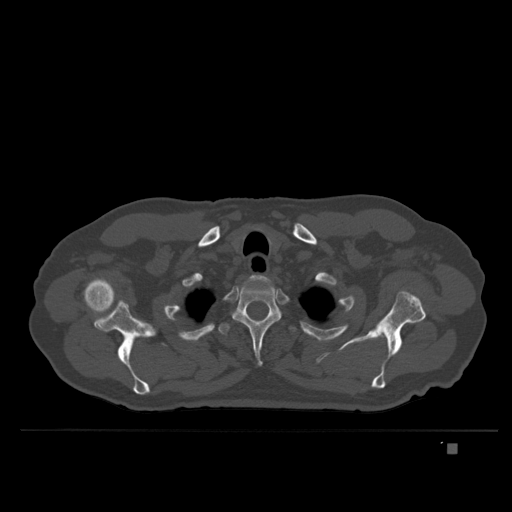
CT including the spine, one axial slice. Position 312 of 435 along the scan axis. Bone window (W 1800 / L 400 HU). 1.5 mm slice thickness. 512 × 512 image matrix, field of view 434 × 434 mm. Patient: male, 73 years. From the clinical record (not read from this slice): primary cancer: skin.
Annotated regions visible in this slice (semi-automatic segmentation, software-assisted and operator-edited):
- T1 vertebra: box from (x=244, y=276) to (x=272, y=284) px
- T2 vertebra: (x=232, y=283)–(x=281, y=366)
- T3 vertebra: (x=218, y=312)–(x=296, y=336)